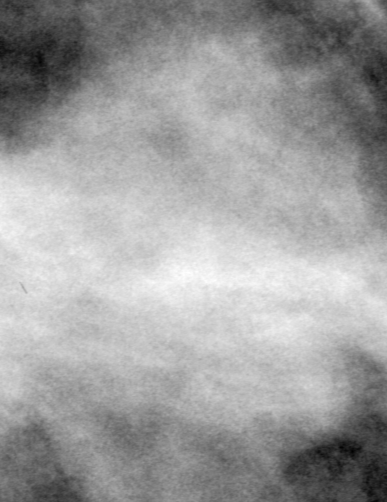
Region of interest cut from a scanned film mammogram (one marked finding), left breast, MLO view, BI-RADS breast density category 3 (scale 1–4).
Marked abnormality: mass, shape lobulated, margins circumscribed; BI-RADS assessment category 0 (incomplete: needs additional imaging); subtlety rating 5 on a 1 (subtle) to 5 (obvious) scale; pathology result (as recorded, not read from the image): benign.